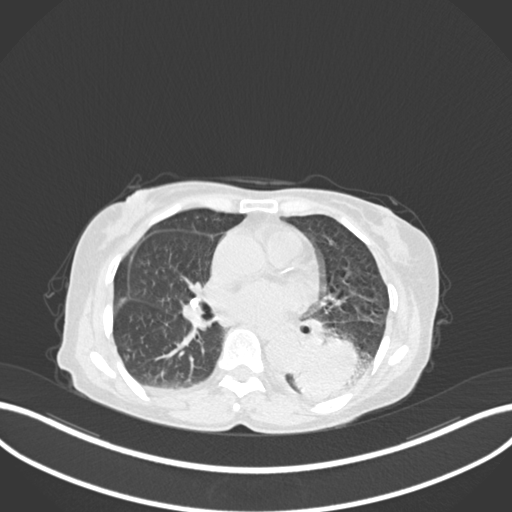
Chest CT, one axial slice; slice 77 of 233 in the series (ordered by position); lung window (W 1500 / L -600 HU); 1 mm slice thickness; 512 × 512 image matrix, field of view 400 × 400 mm. Female patient, age 78 years. Case-level facts recorded for this patient, not image findings: clinical TNM (as recorded): T3 N0 M1.
Annotated regions visible in this slice (bounding box drawn by a radiologist):
- lung tumour (recorded histology: squamous cell carcinoma): bounding box [x1, y1, x2, y2] px = [281, 331, 359, 395]